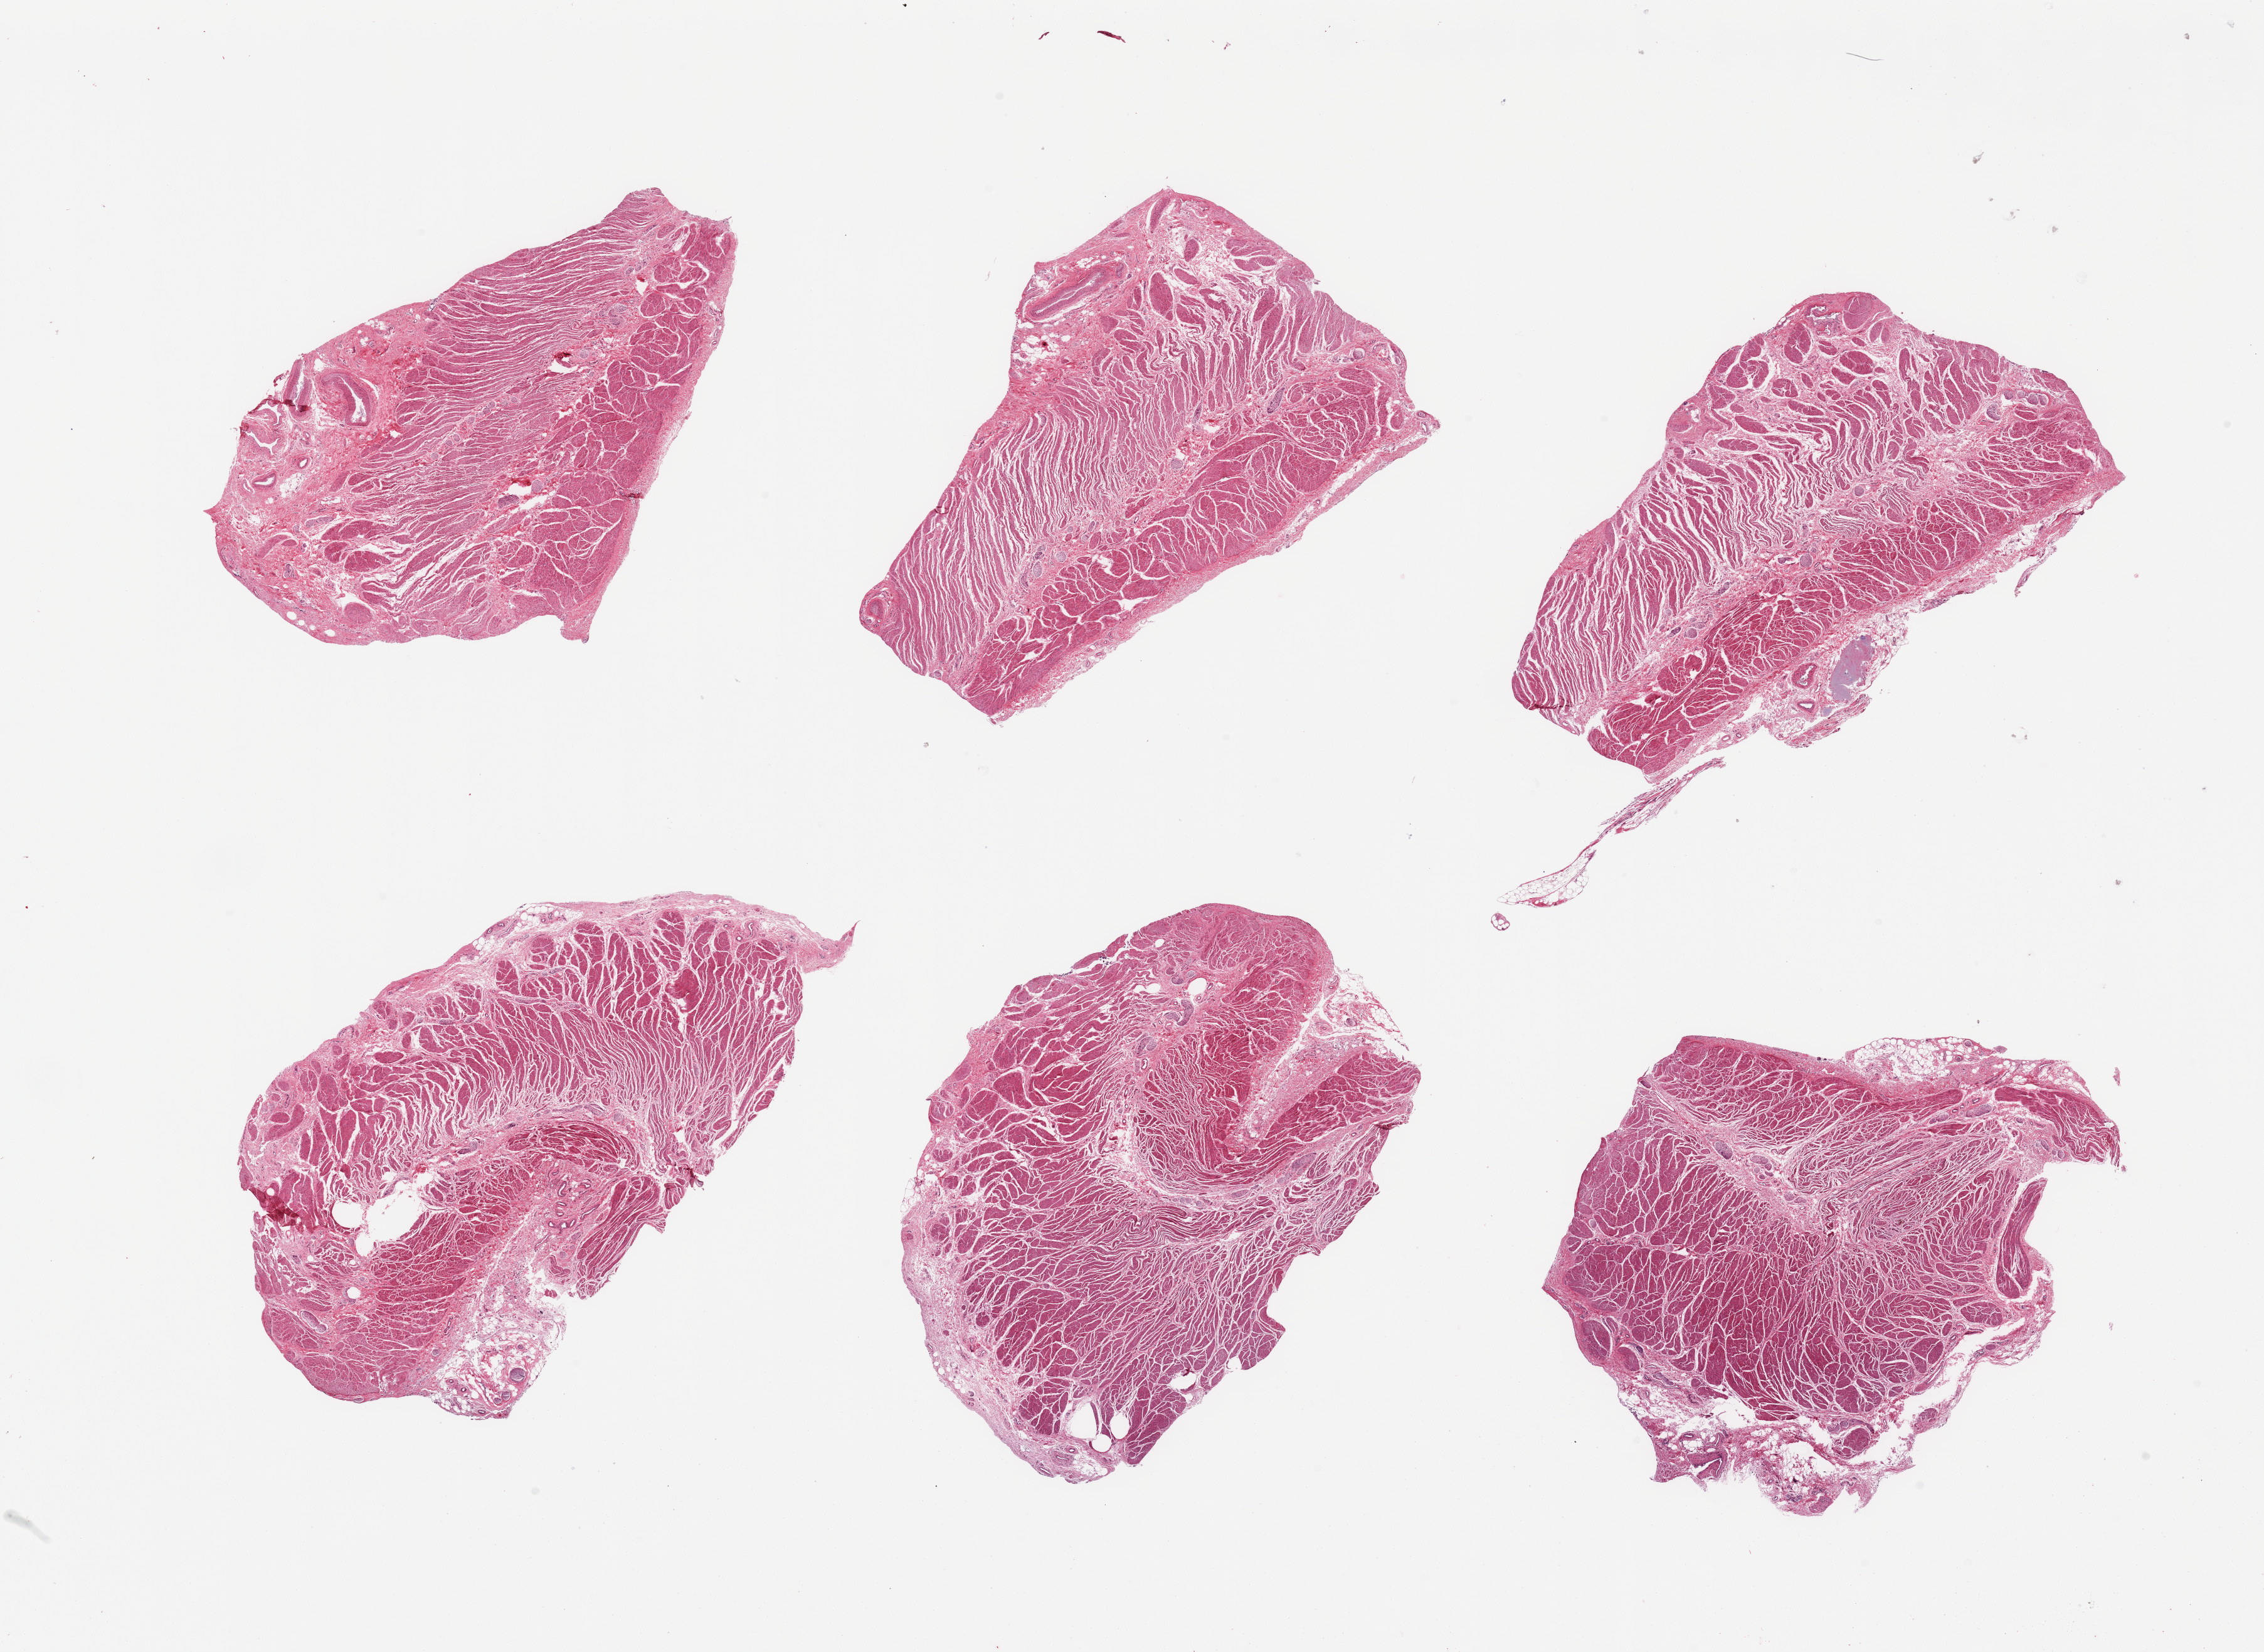
Whole-slide image, hematoxylin and eosin (H&E) stain, whole scanned area (about 28.5 x 20.8 mm, slide scanned at 20x) shown as a low-resolution overview, PAXgene-fixed paraffin-embedded (PFPE) section, target tissue: gastroesophageal junction, tissue donor sample. Donor sex: male.
Review note (as recorded): 6 pieces; well dissected muscularis.